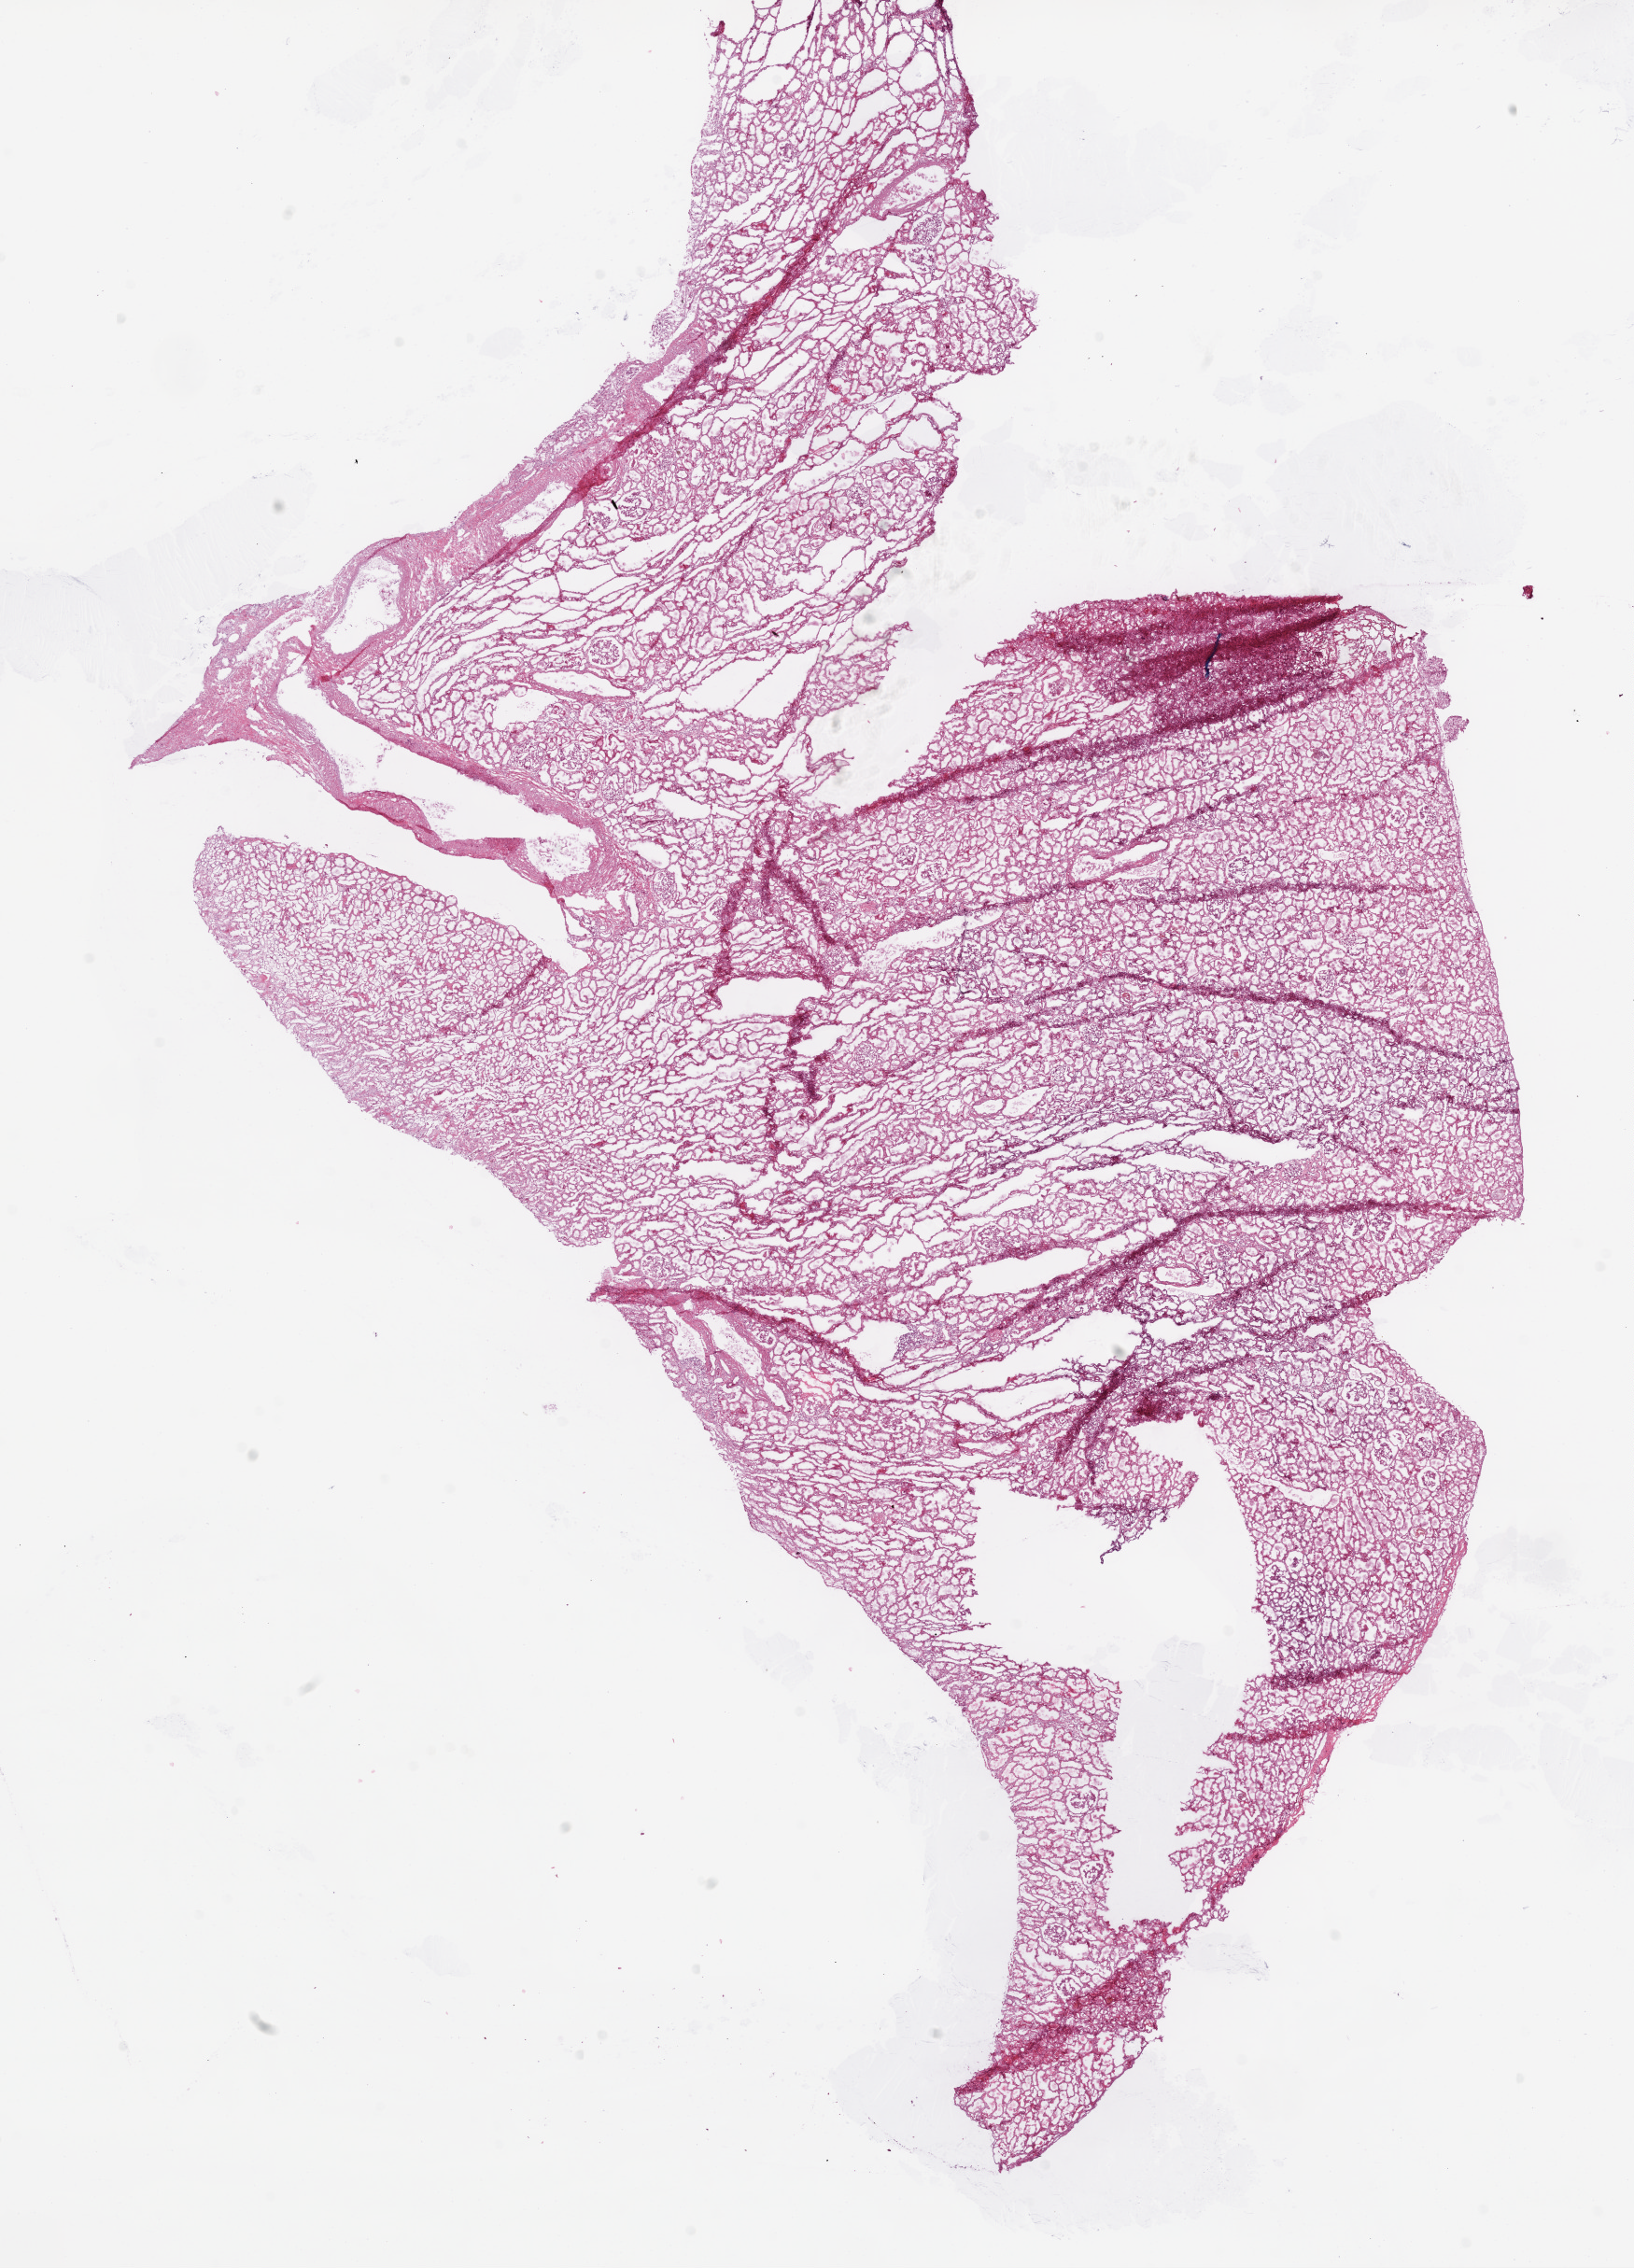
Whole-slide histology image, Hematoxylin and eosin (H&E) stained, whole scanned area (about 14.0 x 19.5 mm) shown as a low-resolution overview; frozen section; sample: solid tissue normal (non-tumour tissue), kidney. Patient: male, age at initial diagnosis 69 years.
This section: solid tissue normal sample (biorepository sample class). Patient diagnosis: Clear cell adenocarcinoma, NOS.